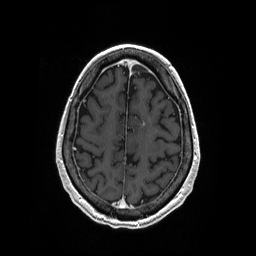
Brain MRI from a brain-tumour surgery series, one axial slice; position 61 of 208 along the scan axis; T1-weighted post-contrast; 1 mm slice thickness; 256 × 256 image matrix. From the clinical record (not read from this slice): histopathology: Primary diffuse large B-cell lymphoma; tumour location: Left Corpus Callosum (Frontal).
Structures marked on this image (expert manual segmentation):
- tumour: bounding box (x1, y1, x2, y2) in pixels: (142, 121, 146, 127)